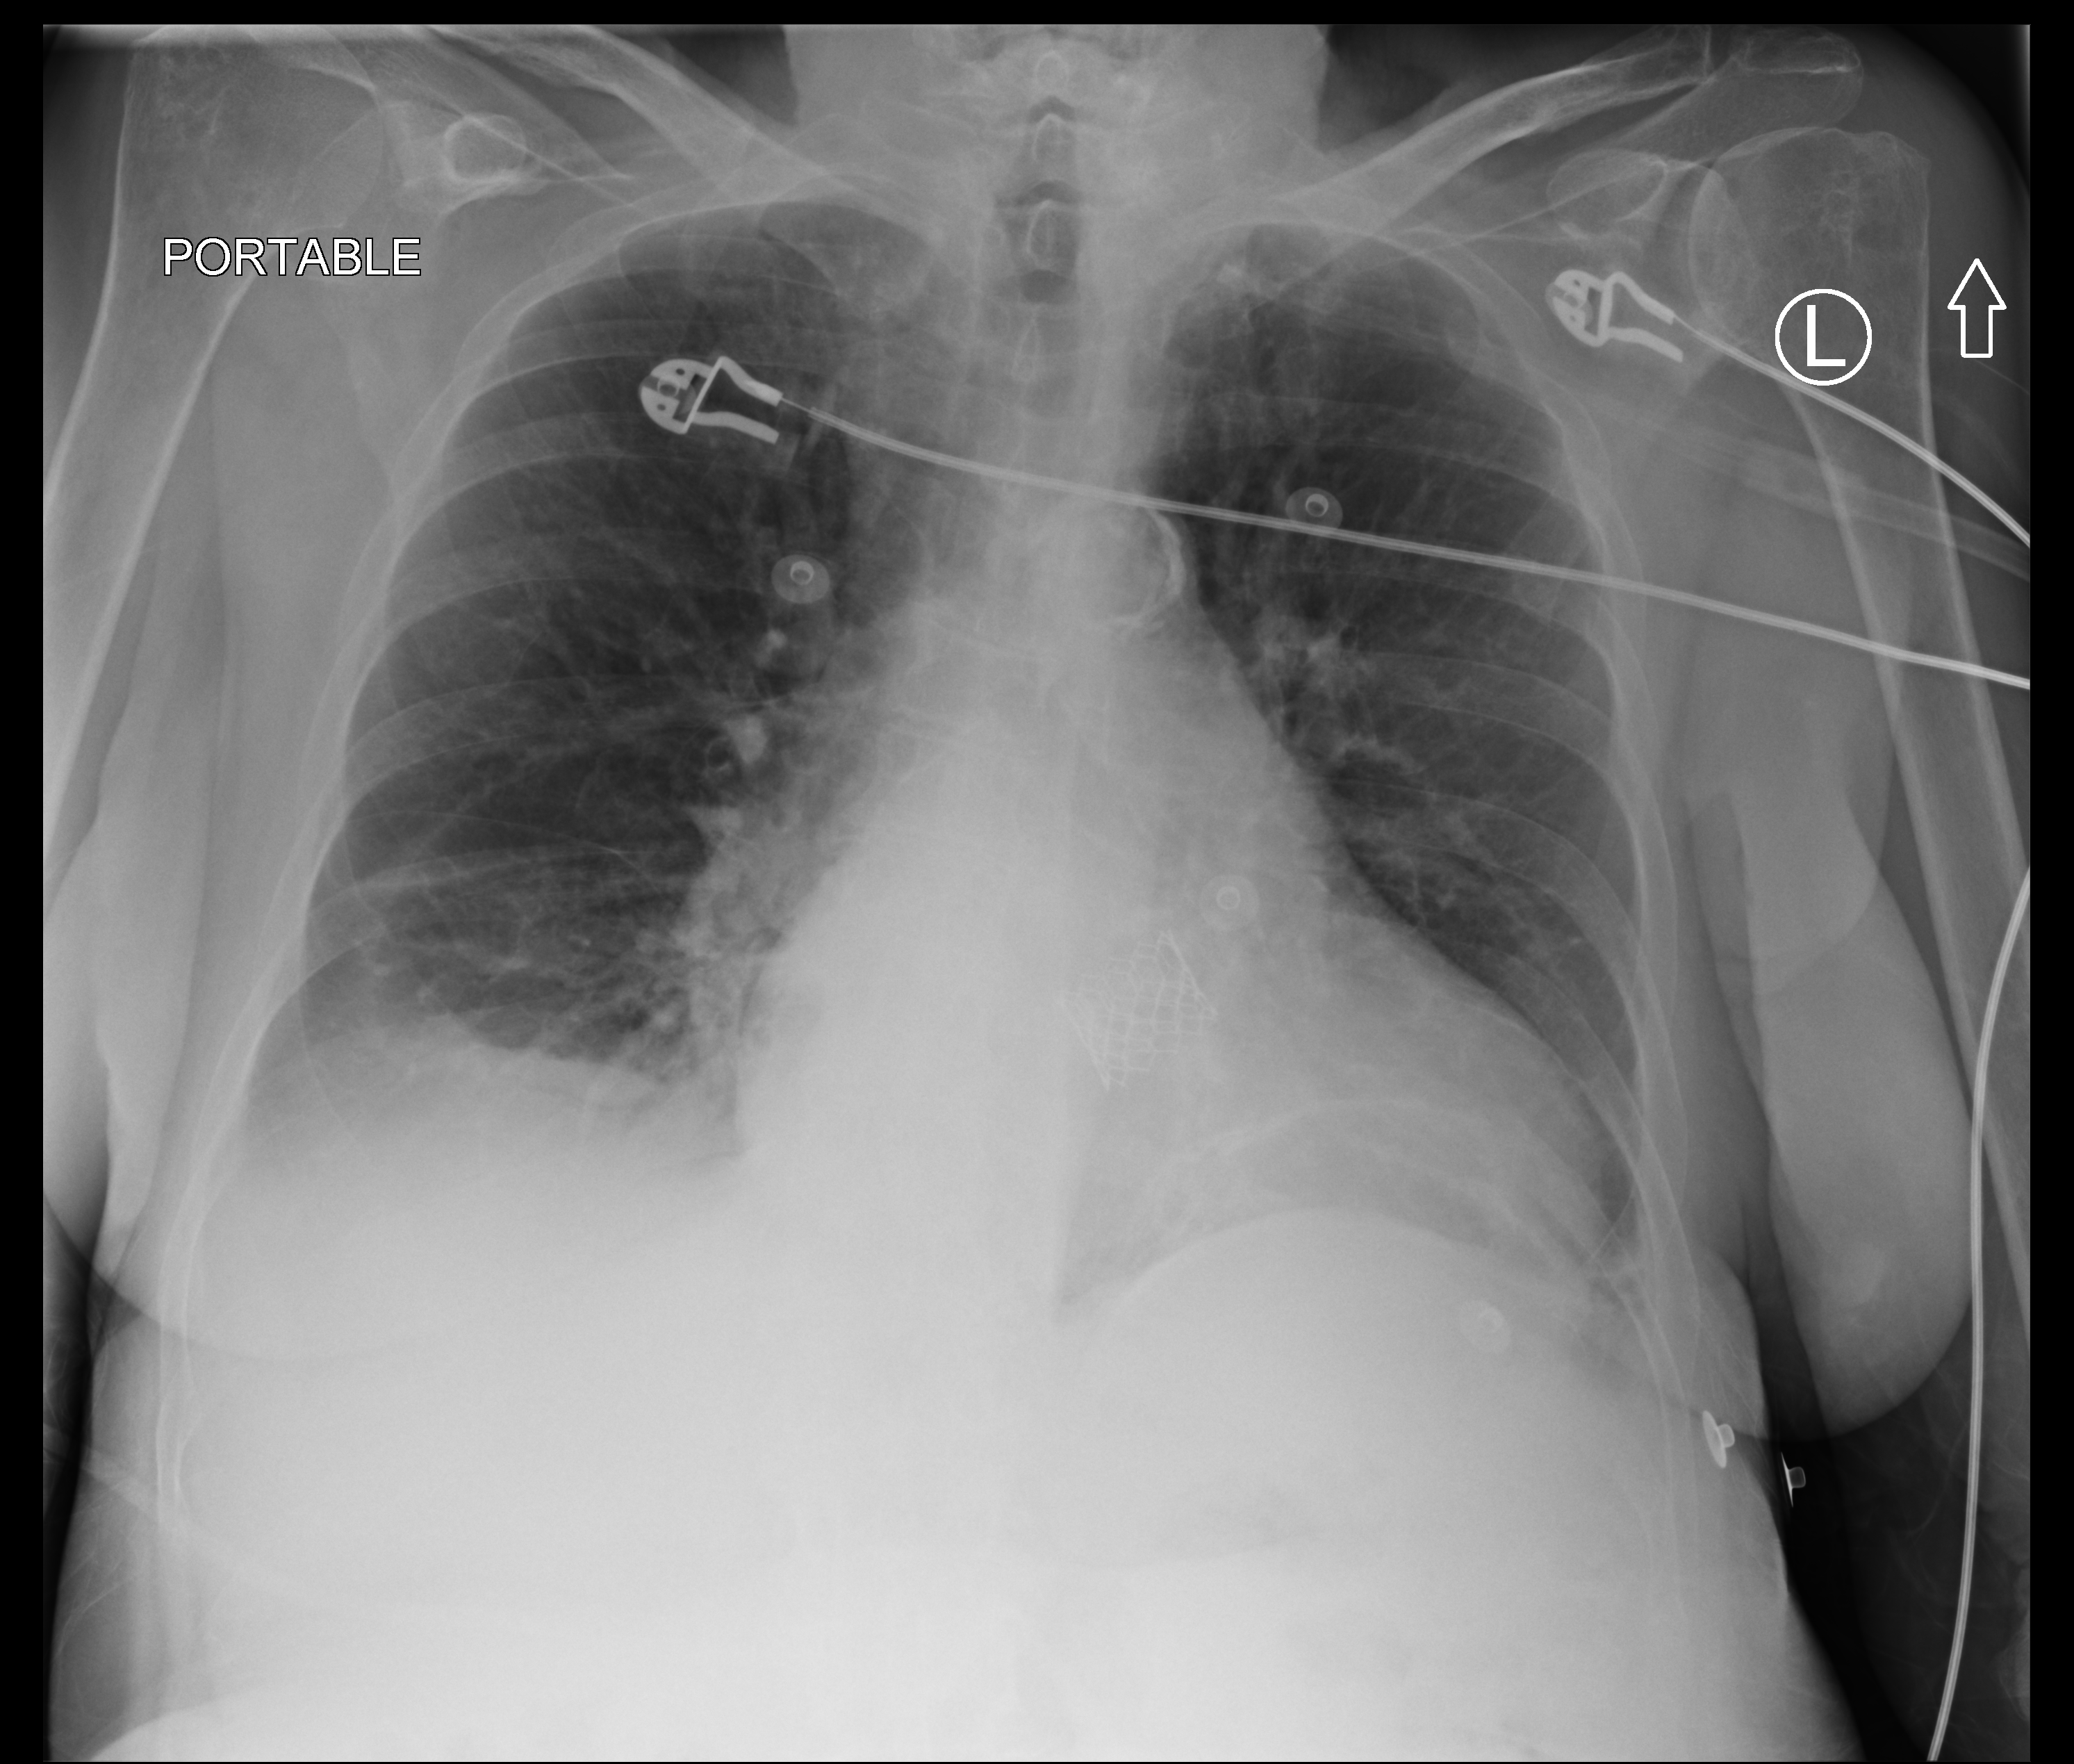
Portable chest radiograph. Patient hospitalised with COVID-19; female, aged 75–90 years.
Admission-level facts for this patient (not findings on this image; timing relative to this image not recorded):
- length of hospital stay: 5 days
- mechanically ventilated during this hospital stay: no